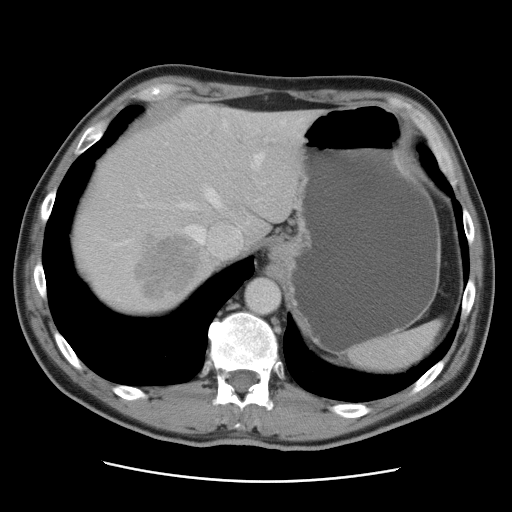
Contrast-enhanced abdominal CT, one axial slice; slice 72 of 89 in the series (ordered by position); 120 kVp; intravenous contrast given; soft-tissue window (W 400 / L 40 HU); 5 mm slice thickness; 512 × 512 image matrix, field of view 366 × 366 mm. Male patient, age 59 years. Case-level facts recorded for this patient, not image findings: diagnosis: colorectal cancer liver metastases, imaged before liver resection; multiple liver metastases: yes; largest metastasis: 0.6 cm; disease in both lobes: yes.
Outlined on this slice (expert manual segmentation):
- hepatic veins: bounding box (x1, y1, x2, y2) in pixels: (140, 120, 302, 256)
- liver: (71, 105, 321, 316)
- planned liver remnant (the part of the liver to remain after resection): (119, 105, 321, 245)
- portal vein (with intrahepatic branches): (265, 139, 268, 141)
- liver metastasis: (137, 237, 200, 298)